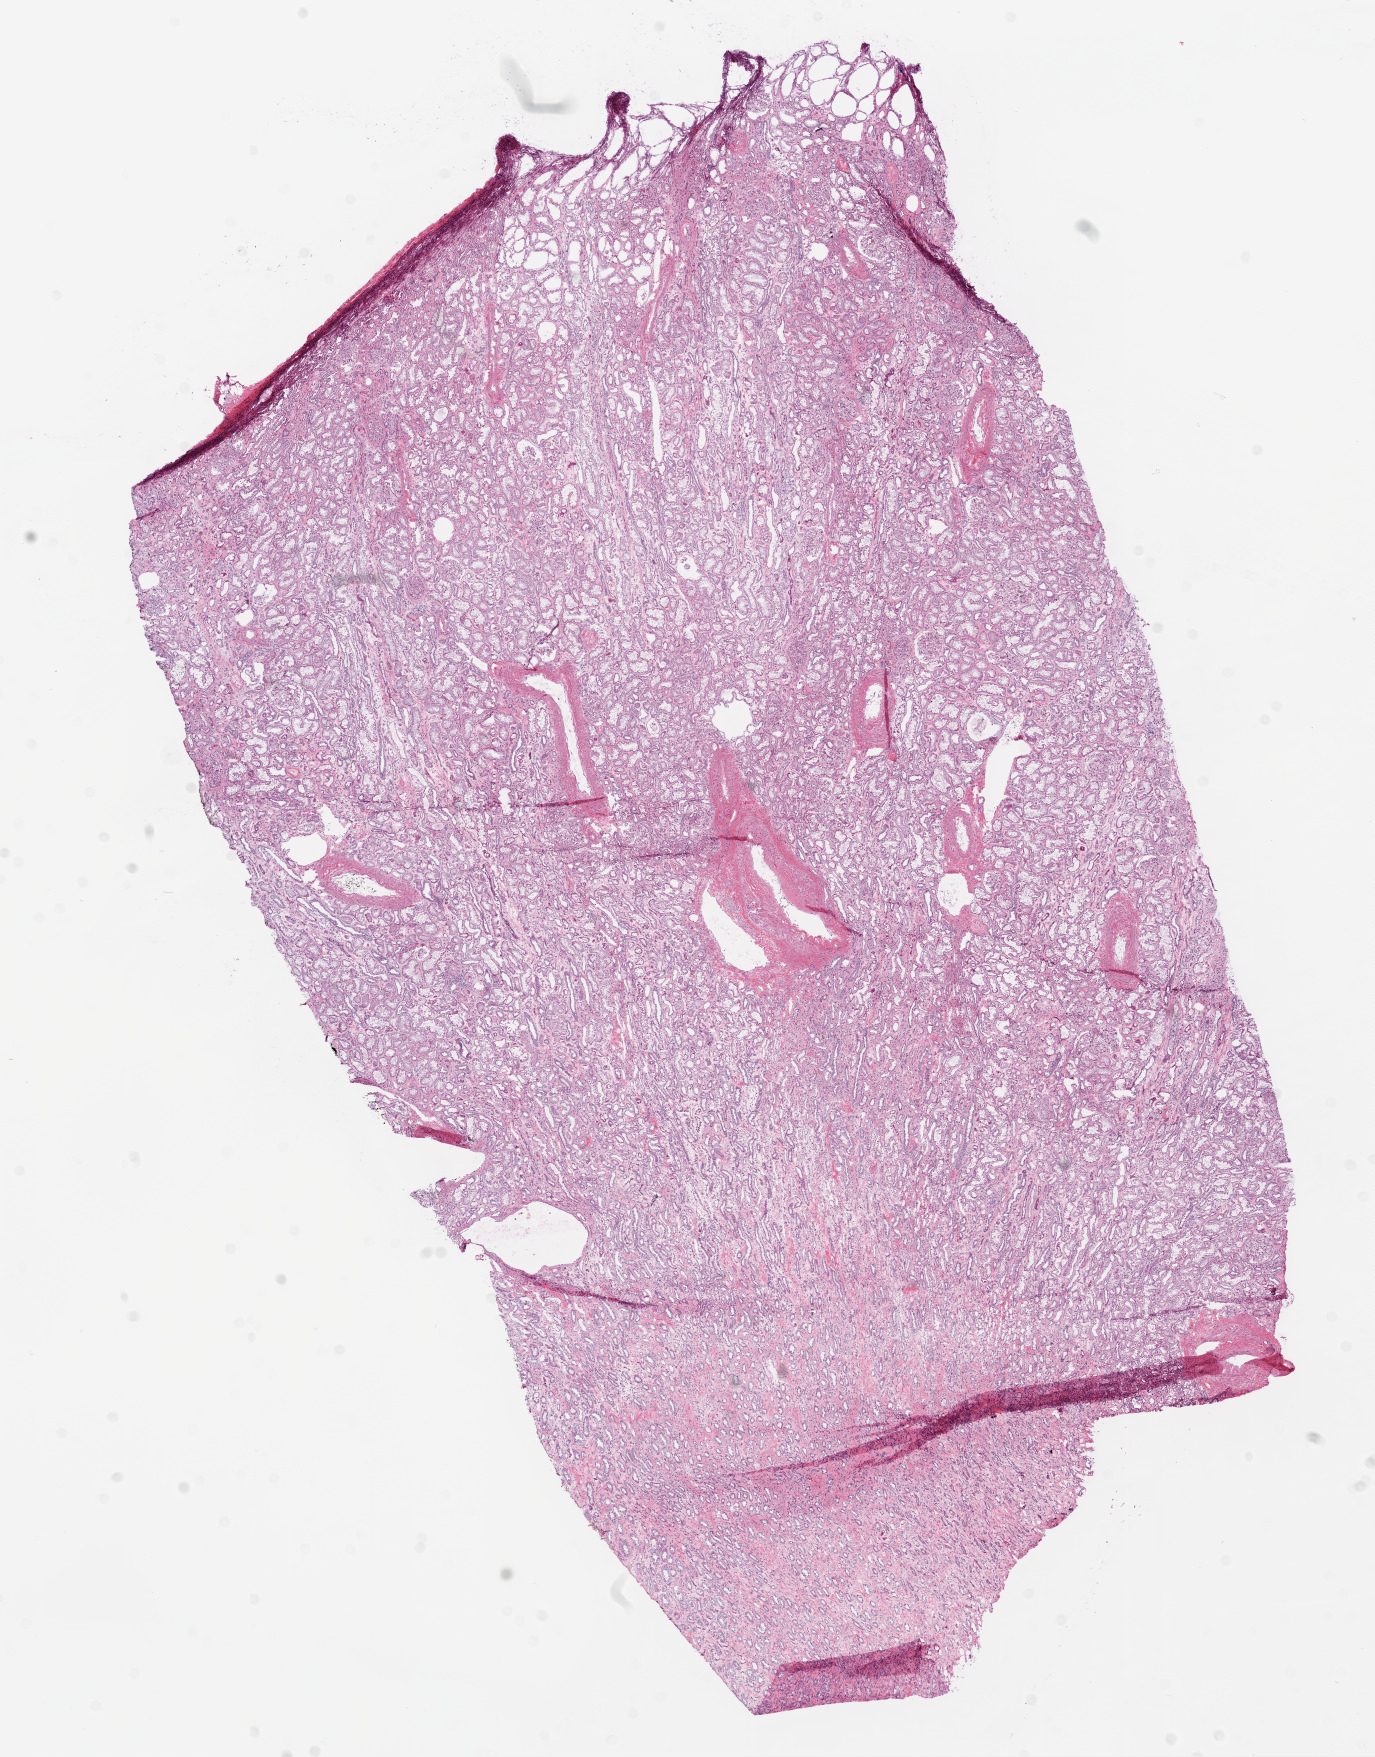
Whole-slide histology image, Hematoxylin and eosin (H&E) stained, shown as a low-resolution overview of the whole scanned area (about 11.0 x 14.1 mm, acquisition: 20x scan), frozen section, sample: solid tissue normal (non-tumour tissue), kidney. Patient: male, age at initial diagnosis 57 years.
• this section: solid tissue normal (non-tumour) sample from the same patient
• patient diagnosis: Clear cell adenocarcinoma, NOS